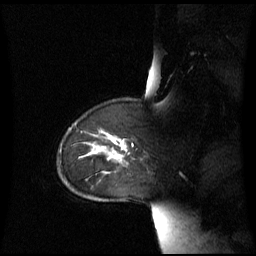
Breast MRI (dynamic contrast-enhanced), one sagittal slice; slice 49 of 60 in the series (ordered by position); dynamic contrast-enhanced series, image 2 of 3 at this slice position (ordered by acquisition); 1.5 T; TE 4.2 ms, TR 8.4 ms; 256 × 256 image matrix, field of view 270 × 270 mm. Female patient, age 43 years. Case-level facts recorded for this patient, not image findings: setting: breast cancer imaged before/during neoadjuvant chemotherapy; receptor status: triple-negative.
Structures marked on this image (semi-automatic segmentation, software-assisted and operator-edited):
- analysis volume of interest (the breast-tissue region the enhancement analysis was run in; not a lesion): bounding box (x1, y1, x2, y2) in pixels: (59, 124, 133, 173)
- tumour enhancement mask (voxels above the 70 % enhancement threshold inside the analysis volume of interest): (109, 137, 124, 147)